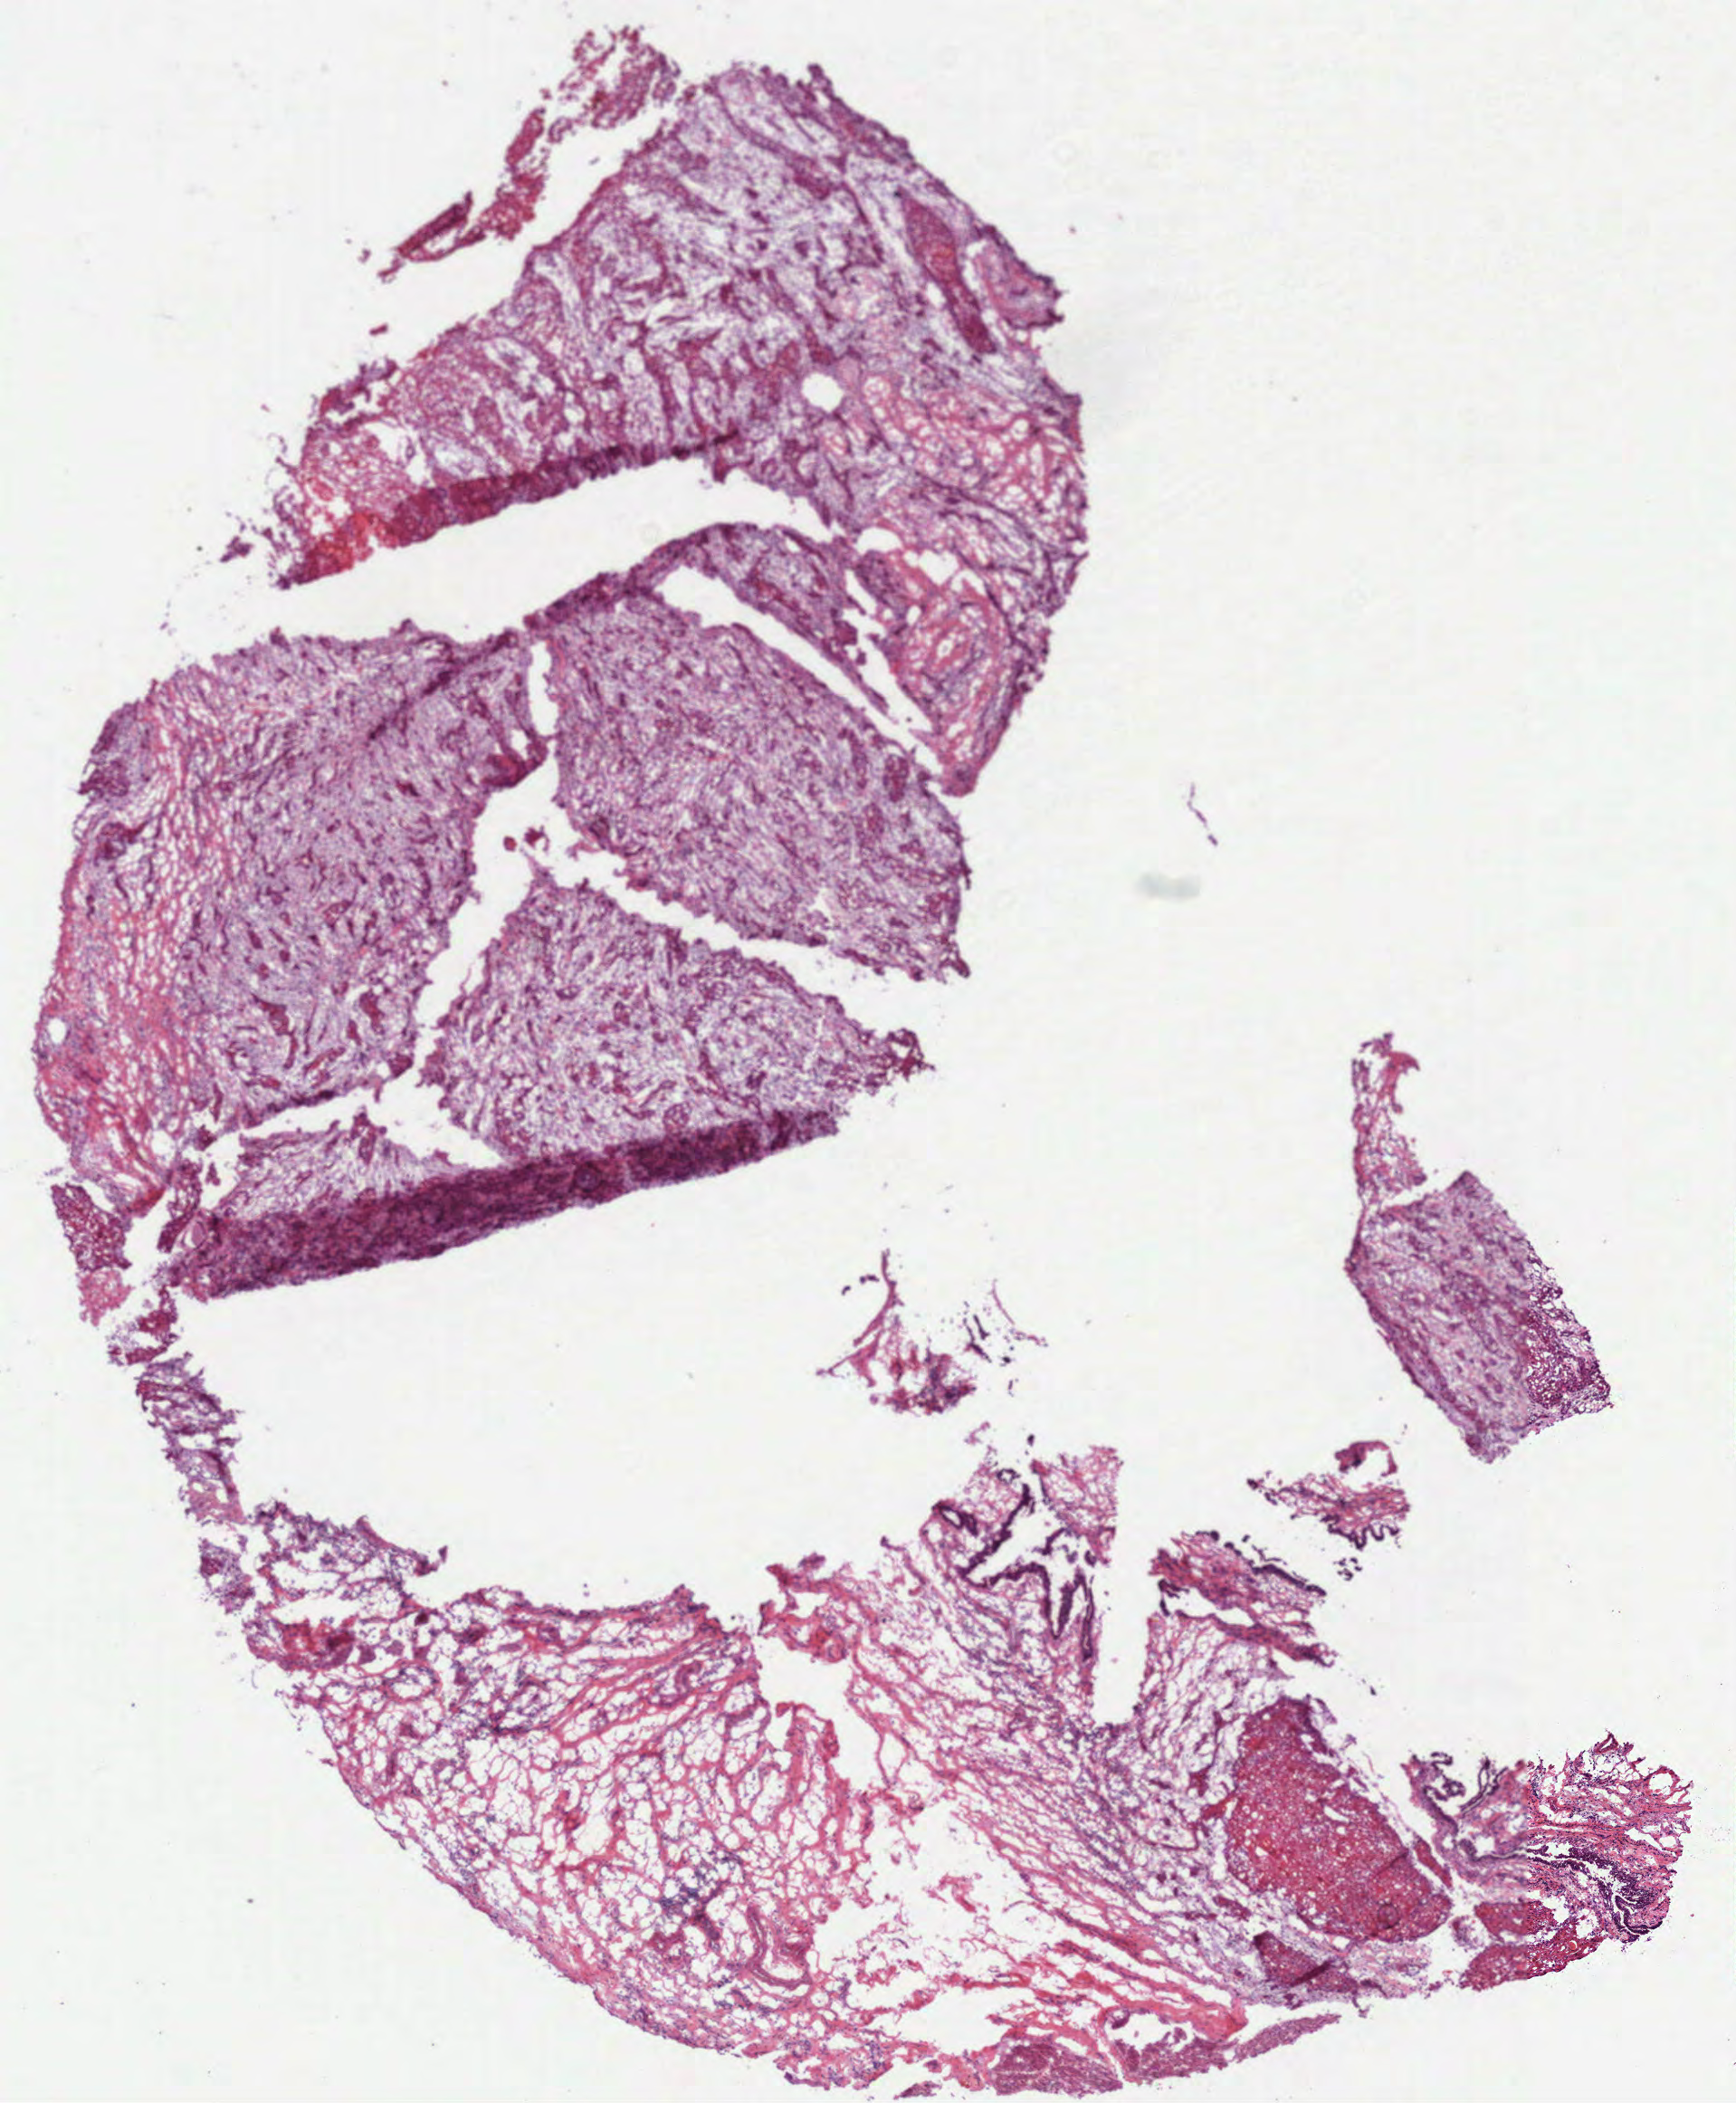
Whole-slide histology image, Hematoxylin and eosin (H&E) stained, whole scanned area (about 7.7 x 9.4 mm) shown as a low-resolution overview; frozen section from the top of the tissue portion; head and neck, primary tumour sample. Patient: female, age at initial diagnosis 77 years. Histologic grade: G3 (poorly differentiated). Slide review estimates, as recorded: tumour cells 60%, tumour nuclei 60%, normal cells 0%, stromal cells 40%, necrosis 0%.
Lymph nodes positive (case pathology): 6 of 34 examined. AJCC pathologic stage: IVA (7th edition). Diagnosis: Squamous cell carcinoma, NOS (tongue, NOS). TNM: T3 N2c.